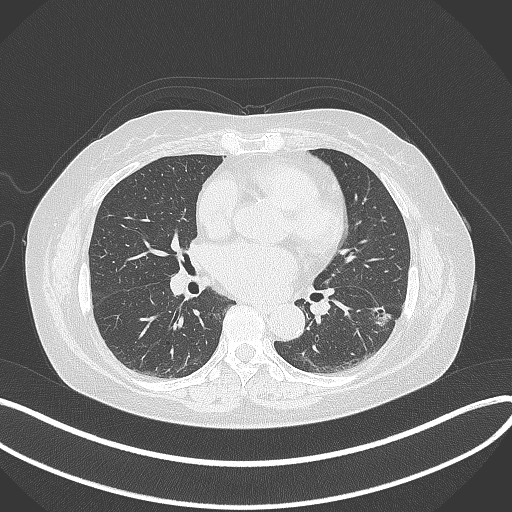
Chest CT, one axial slice. Slice 174 of 373 in the series (ordered by position). Reconstruction kernel B70f. 120 kVp. Lung window (W 1500 / L -600 HU). 512 × 512 image matrix, field of view 400 × 400 mm. Female patient, age 67 years. From the clinical record (not read from this slice): clinical TNM (as recorded): T1c N0 M0; histopathological grade: G2.
Outlined on this slice (rectangle marked by the reading radiologist):
- lung tumour (recorded histology: adenocarcinoma): bounding box [x1, y1, x2, y2] px = [365, 296, 395, 329]